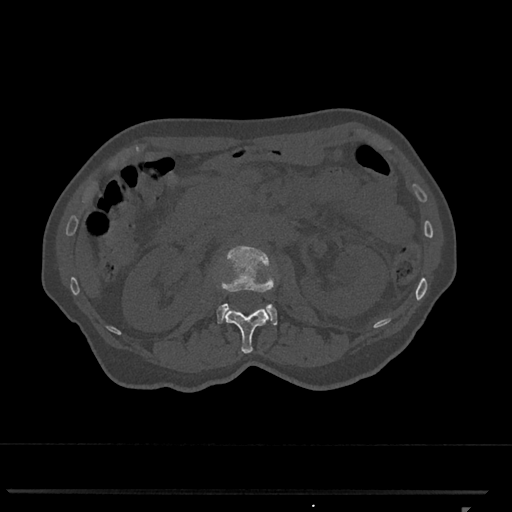
CT including the spine, one axial slice. 120 kVp. Bone window (W 1800 / L 400 HU). 0.5 mm slice thickness. 512 × 512 image matrix, field of view 380 × 380 mm. Female patient, age 62 years. Case-level facts recorded for this patient, not image findings: primary cancer: renal.
Outlined on this slice (semi-automatically segmented with operator editing):
- L1 vertebra: bounding box (x1, y1, x2, y2) in pixels: (225, 308, 270, 354)
- L2 vertebra: (217, 246, 278, 326)